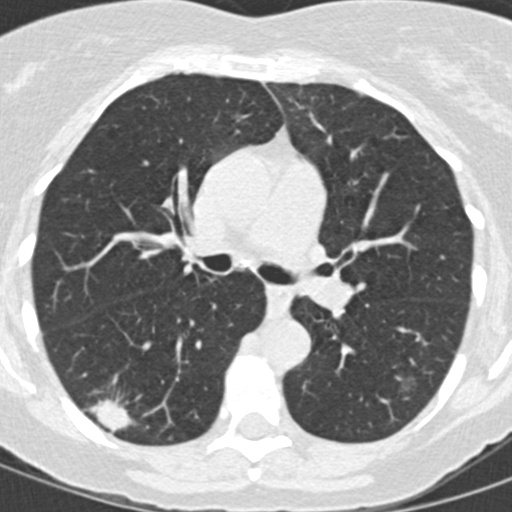
Low-dose screening chest CT, one axial slice. Slice 87 of 146 in the series (ordered by position). Reconstruction kernel B30f. 120 kVp. Lung window (W 1500 / L -600 HU). 2 mm slice thickness. 512 × 512 image matrix, field of view 270 × 270 mm.
Annotated regions visible in this slice (expert manual segmentation):
- lesion 1 (tumor, lower lobe of right lung): bounding box (x1, y1, x2, y2) in pixels: (90, 399, 134, 431)